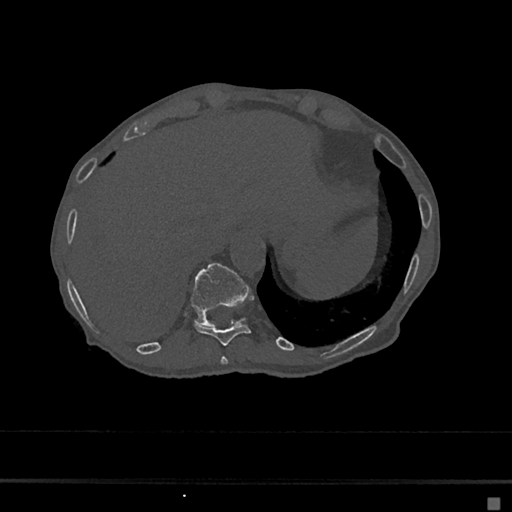
CT including the spine, one axial slice. Slice 208 of 797 in the series (ordered by position). Bone window (W 1800 / L 400 HU). 0.5 mm slice thickness. 512 × 512 image matrix, field of view 360 × 360 mm. Patient: female, 68 years. Case-level facts recorded for this patient, not image findings: primary cancer: renal.
Annotated regions visible in this slice (semi-automatically segmented with operator editing):
- T10 vertebra: bounding box <194,324,251,346> (left, top, right, bottom; pixels)
- T11 vertebra: <191,263,250,326>
- T9 vertebra: <221,356,228,365>